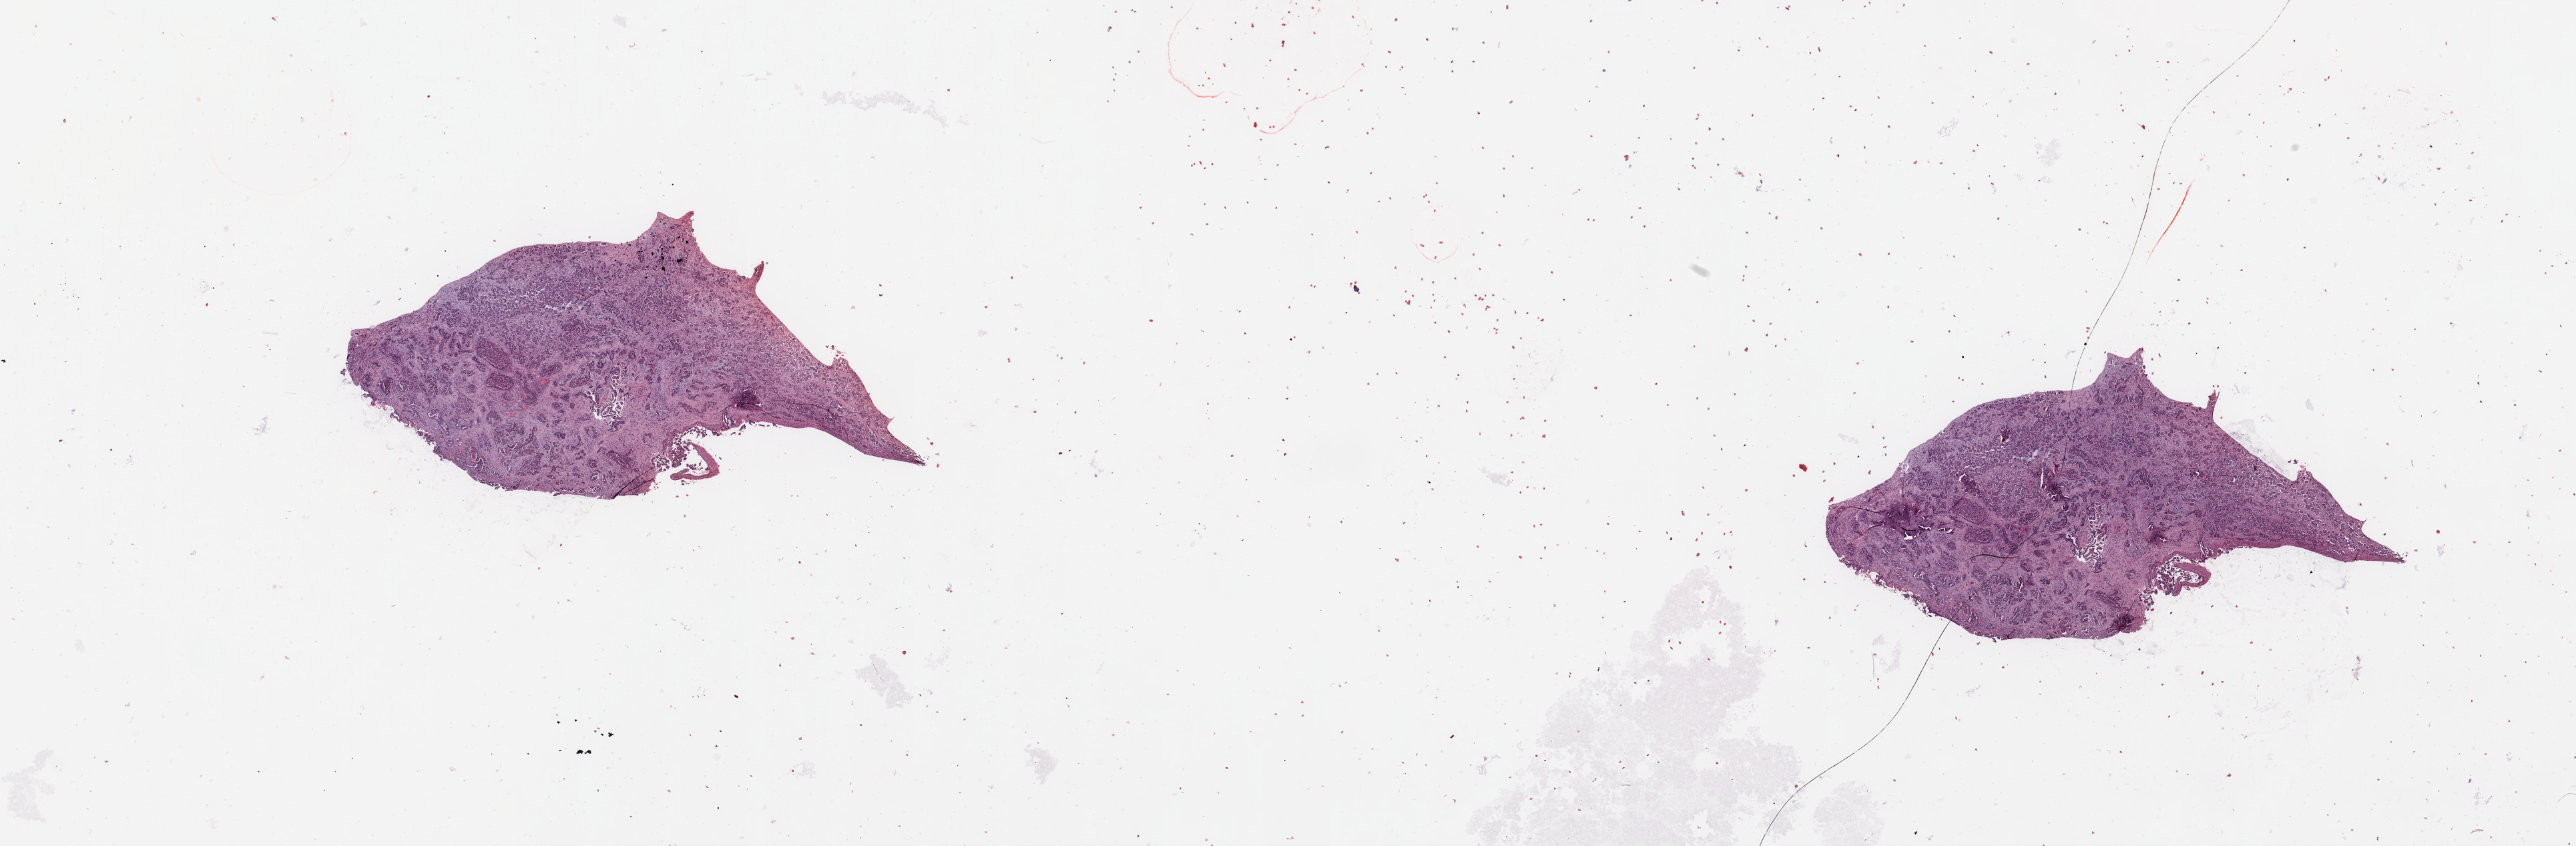
Digitized H&E-stained tissue section (whole slide), a low-resolution overview of the entire scanned area, about 30.5 x 10.0 mm (slide scanned at 20x), tumour tissue sample, sampled site: lung. Patient: male, age 39 years. Histologic grade: G2 (moderately differentiated). Slide review estimates, as recorded: tumour nuclei 80%, necrosis 0%.
AJCC pathologic stage: IIIA. Histologic diagnosis: Adenocarcinoma, NOS.